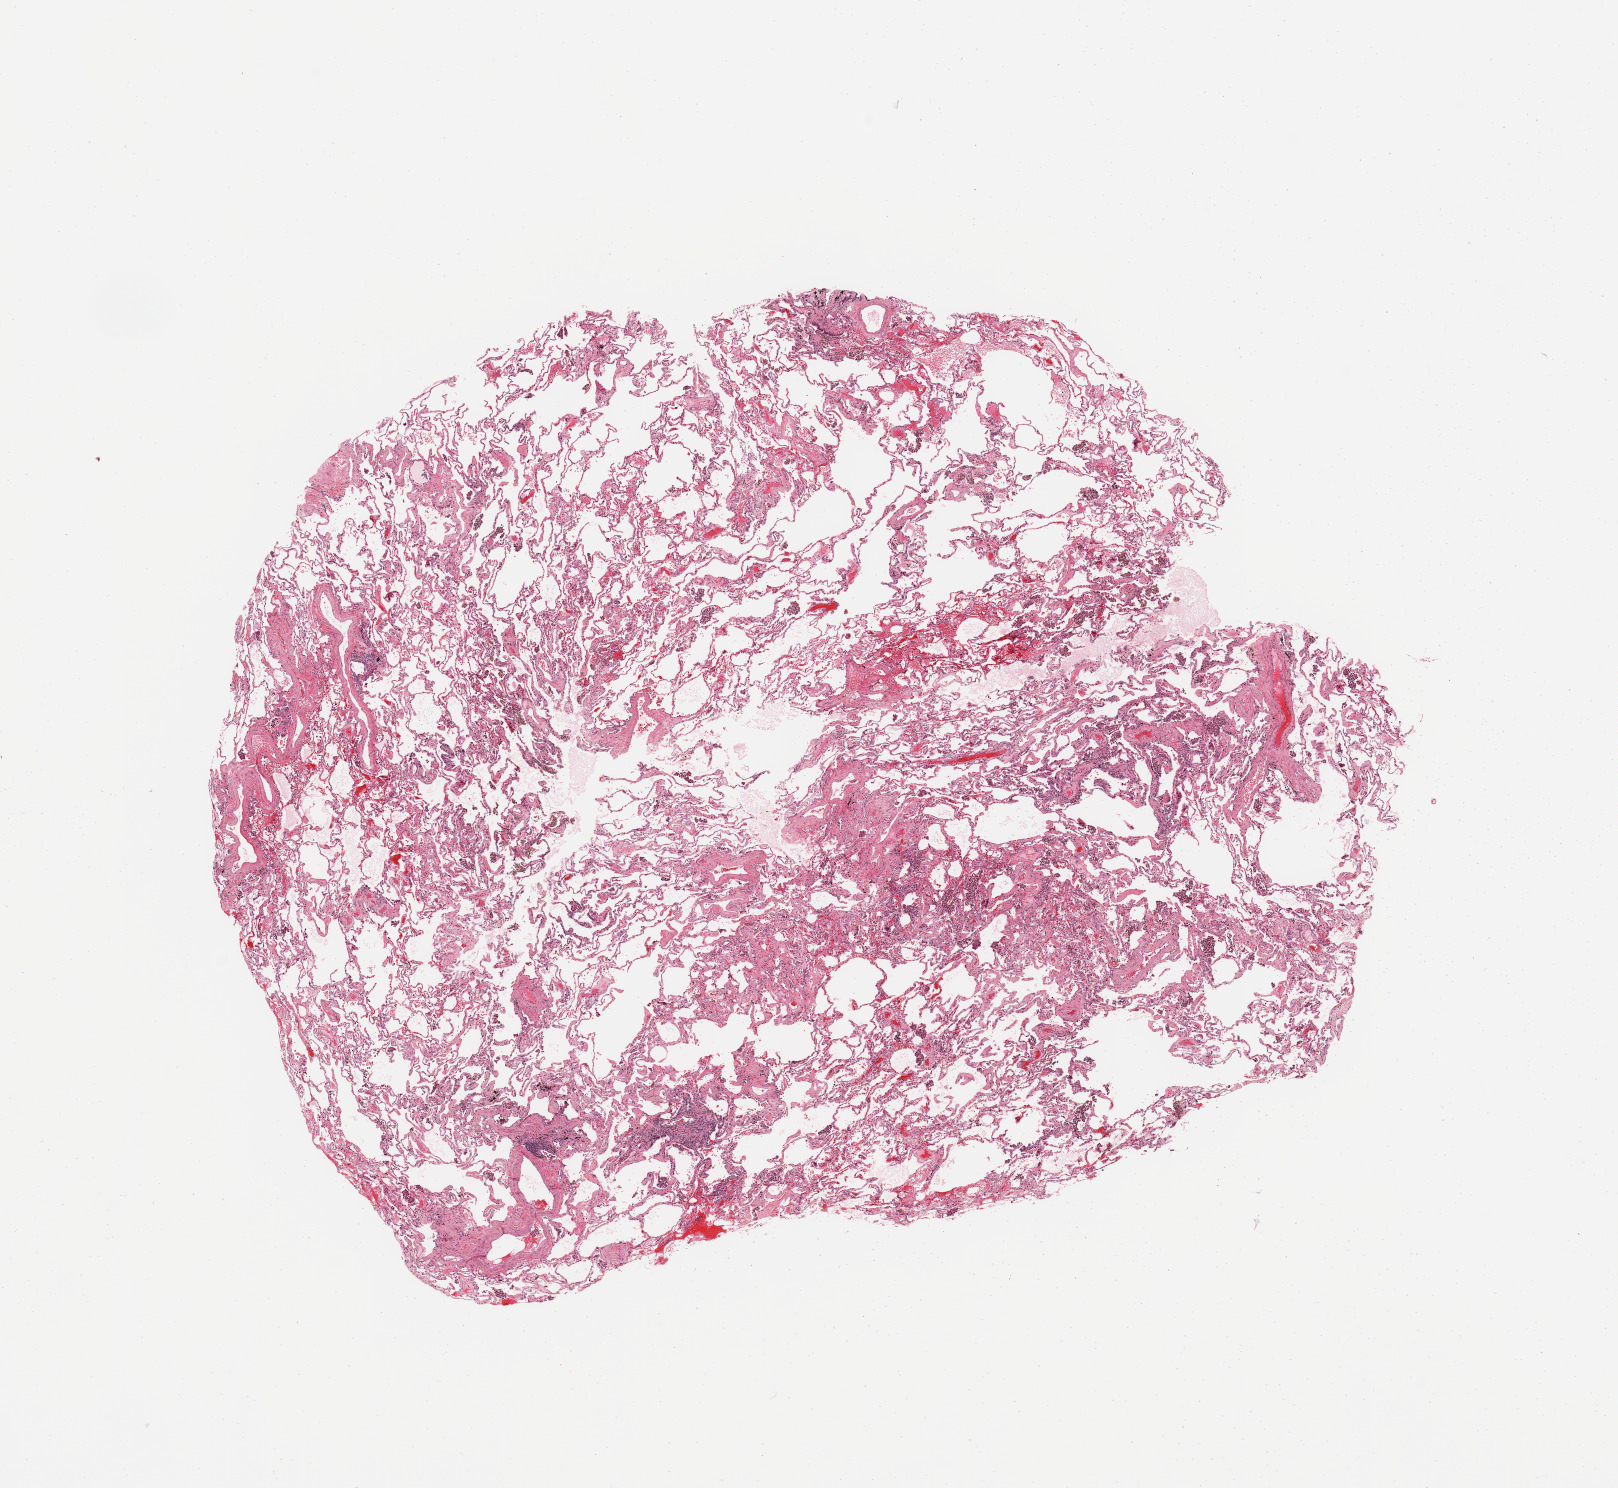
Digitized H&E tissue section (whole slide) — shown as a low-resolution overview of the whole scanned area (about 12.8 x 11.8 mm, from a 20x scan); normal (non-tumour) tissue sample, sampled site: lung. Patient: male, age 74 years.
This section: normal (non-tumour) tissue from the same patient. Patient diagnosis: Squamous cell carcinoma, NOS.